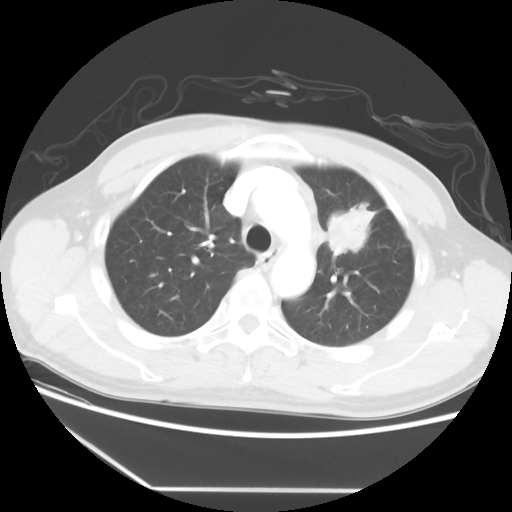
Chest CT, one axial slice; slice 40 of 56 in the series (ordered by position); 120 kVp; lung window (W 1500 / L -600 HU); 5 mm slice thickness; 512 × 512 image matrix, field of view 373 × 373 mm. Male patient, age 53 years. Case-level facts recorded for this patient, not image findings: clinical TNM (as recorded): T2a N1 M1b.
Structures marked on this image (bounding box drawn by a radiologist):
- lung tumour (recorded histology: adenocarcinoma): bounding box <326,197,375,263> (left, top, right, bottom; pixels)